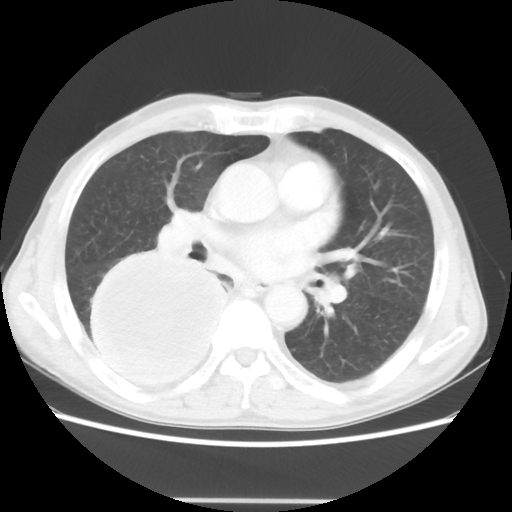
Chest CT, one axial slice. Slice 24 of 48 in the series (ordered by position). Reconstruction kernel STANDARD. 100 kVp. Lung window (W 1500 / L -600 HU). 512 × 512 image matrix, field of view 361 × 361 mm. Patient: male, 66 years. From the clinical record (not read from this slice): clinical TNM (as recorded): T4 N1 M1; histopathological grade: G3.
Structures marked on this image (bounding box drawn by a radiologist):
- lung tumour (recorded histology: small cell carcinoma): bounding box [x1, y1, x2, y2] px = [84, 244, 234, 395]